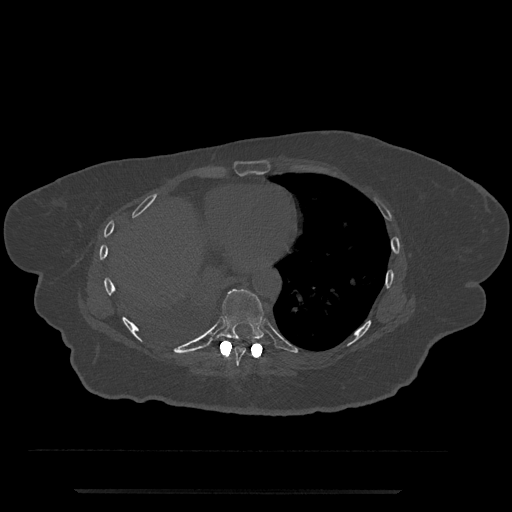
CT including the spine, one axial slice; slice 359 of 797 in the series (ordered by position); reconstruction kernel Br40s/3; bone window (W 1800 / L 400 HU); 512 × 512 image matrix, field of view 440 × 440 mm. Female patient, age 51 years. From the clinical record (not read from this slice): primary cancer: neuro.
Outlined on this slice (semi-automatically segmented with operator editing):
- T8 vertebra: bounding box [x1, y1, x2, y2] px = [230, 347, 249, 366]
- T9 vertebra: [212, 289, 264, 342]